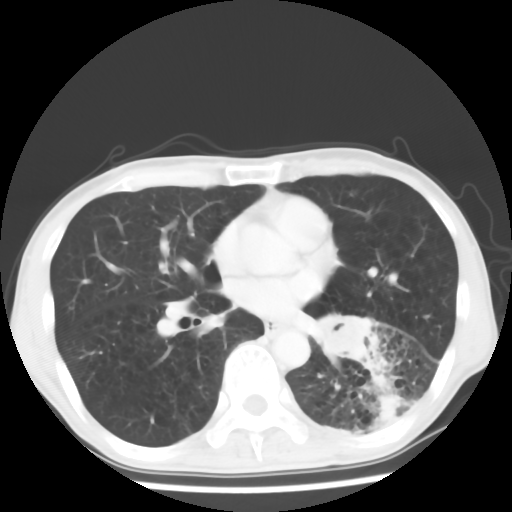
Chest CT, one axial slice. Position 30 of 64 along the scan axis. 120 kVp. Lung window (W 1500 / L -600 HU). 5 mm slice thickness. 512 × 512 image matrix. Patient: male, 68 years. Case-level facts recorded for this patient, not image findings: clinical TNM (as recorded): T4 N0 M0.
Outlined on this slice (bounding box drawn by a radiologist):
- lung tumour (recorded histology: squamous cell carcinoma): bounding box [x1, y1, x2, y2] px = [313, 307, 385, 373]